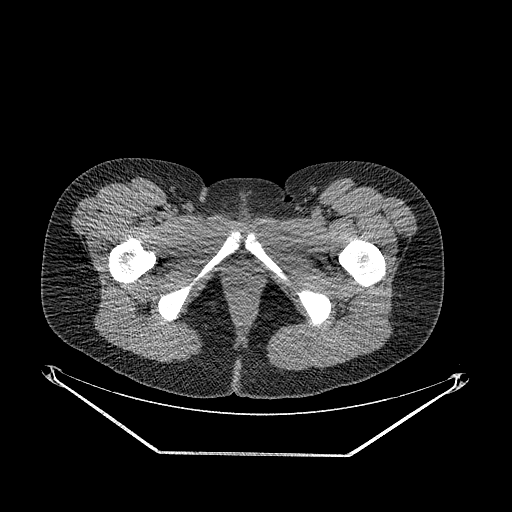
CT of an extremity soft-tissue mass (from a PET/CT study), one axial slice. Position 36 of 267 along the scan axis. Reconstruction kernel STANDARD. 120 kVp. Soft-tissue window (W 400 / L 40 HU). 3.75 mm slice thickness. 512 × 512 image matrix, field of view 500 × 500 mm. Female patient. From the clinical record (not read from this slice): histological type: epithelioid sarcoma; grade: intermediate; site of the primary tumour: right buttock.
Outlined on this slice (expert contour drawn on MRI and transferred to this co-registered scan by the dataset authors):
- gross tumour volume including surrounding oedema: box from (x=189, y=299) to (x=213, y=325) px